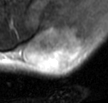
MRI of an extremity soft-tissue mass, one axial slice; slice 26 of 42 in the series (ordered by position); T2-weighted fat-saturated; MR volume resampled by the dataset authors to the PET/CT grid (not the native acquisition matrix); 108 × 103 image matrix. Male patient. From the clinical record (not read from this slice): histological type: leiomyosarcoma; grade: intermediate; site of the primary tumour: left pelvis.
Structures marked on this image (expert contour drawn on MRI and transferred to this co-registered scan by the dataset authors):
- gross tumour volume (mass): bounding box <23,23,86,72> (left, top, right, bottom; pixels)